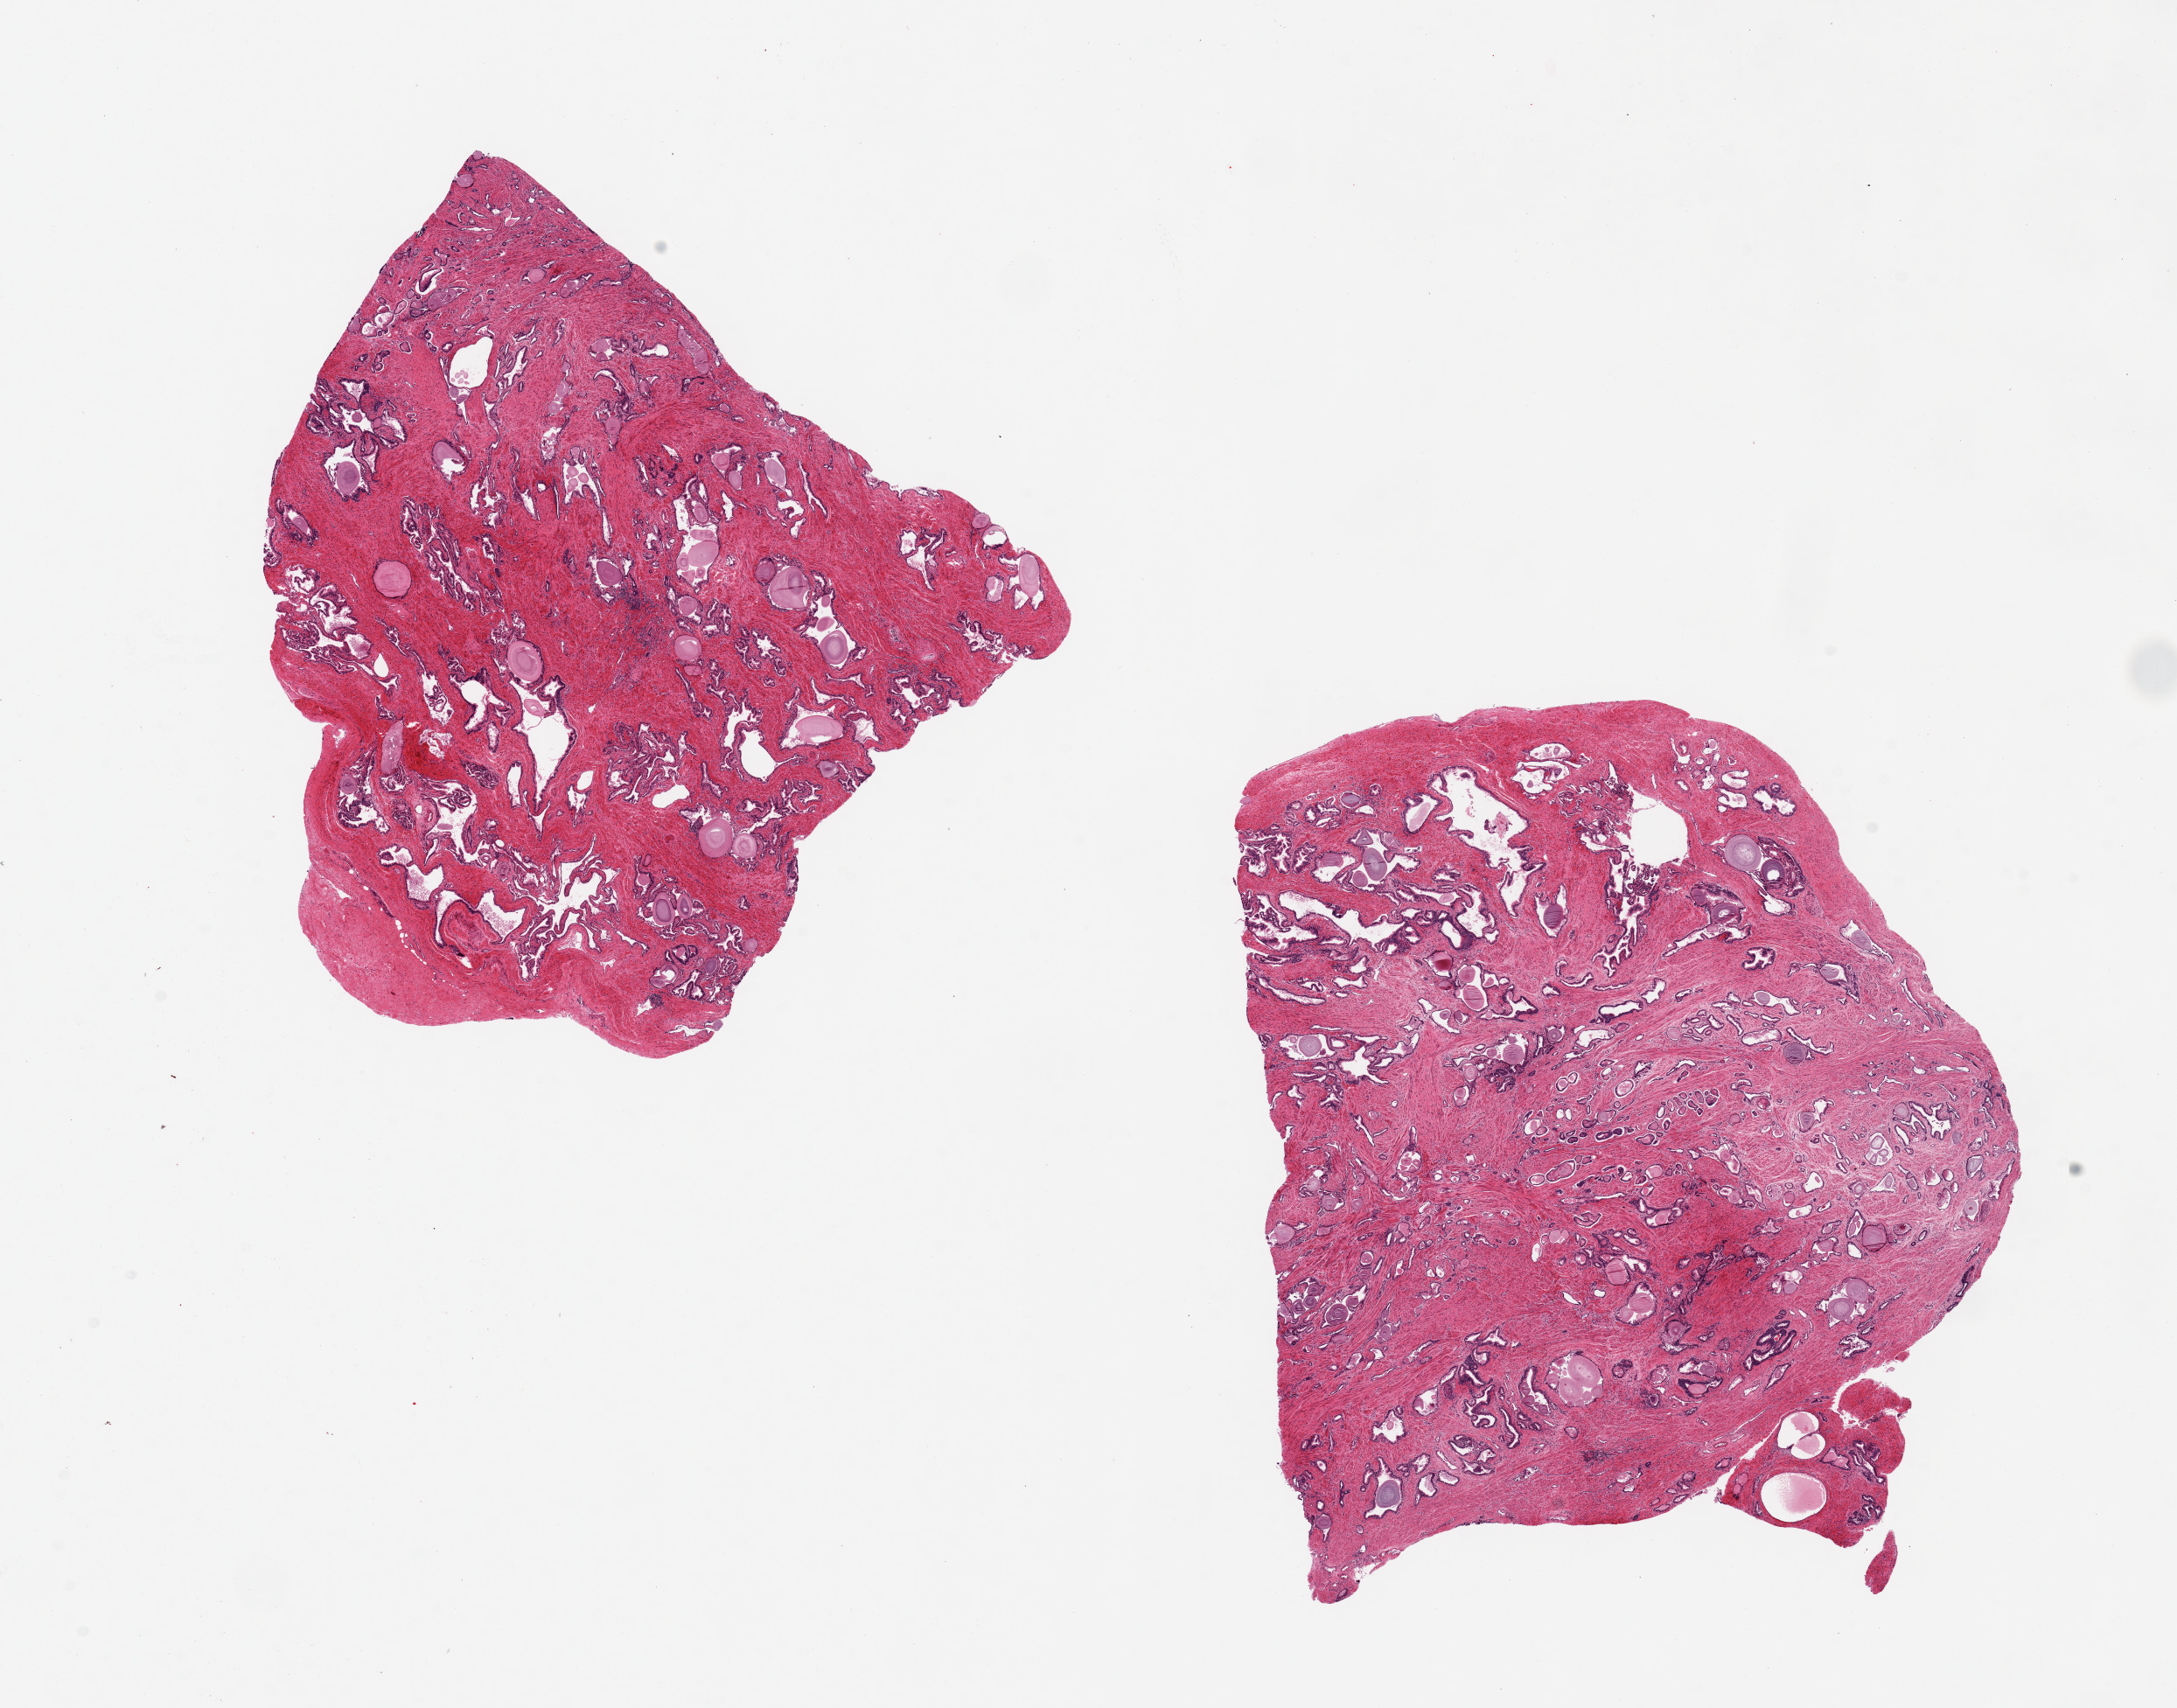
Hematoxylin and eosin (H&E) whole-slide image, brightfield — a low-resolution overview of the entire scanned area, about 19.7 x 15.4 mm. PAXgene-fixed, paraffin-embedded tissue. Sampled site (target tissue): prostate. Donor tissue sample. Donor sex: male.
Pathologist's review note for this sample: 2 pieces, 7.5x7 & 9x8mm; hyperplasia.